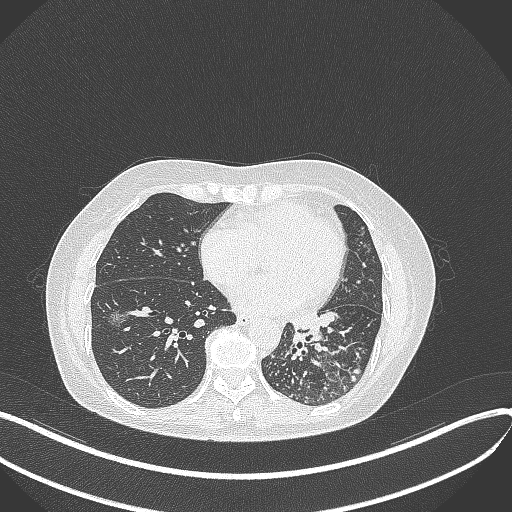
Chest CT, one axial slice; position 159 of 429 along the scan axis; 100 kVp; lung window (W 1500 / L -600 HU); 1 mm slice thickness; 512 × 512 image matrix, field of view 400 × 400 mm. Patient: female, 63 years. From the clinical record (not read from this slice): clinical TNM (as recorded): T1b N0 M0; histopathological grade: G2-3.
Outlined on this slice (bounding box drawn by a radiologist):
- lung tumour (recorded histology: adenocarcinoma): bounding box <284,306,325,347> (left, top, right, bottom; pixels)